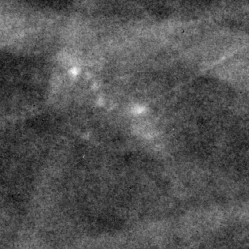
Region of interest cut from a scanned film mammogram (one marked finding), right breast, CC view.
Marked abnormality: calcifications, morphology pleomorphic, distribution clustered; BI-RADS assessment category 4; subtlety rating 3 on a 1 (subtle) to 5 (obvious) scale; pathology (as recorded): benign.